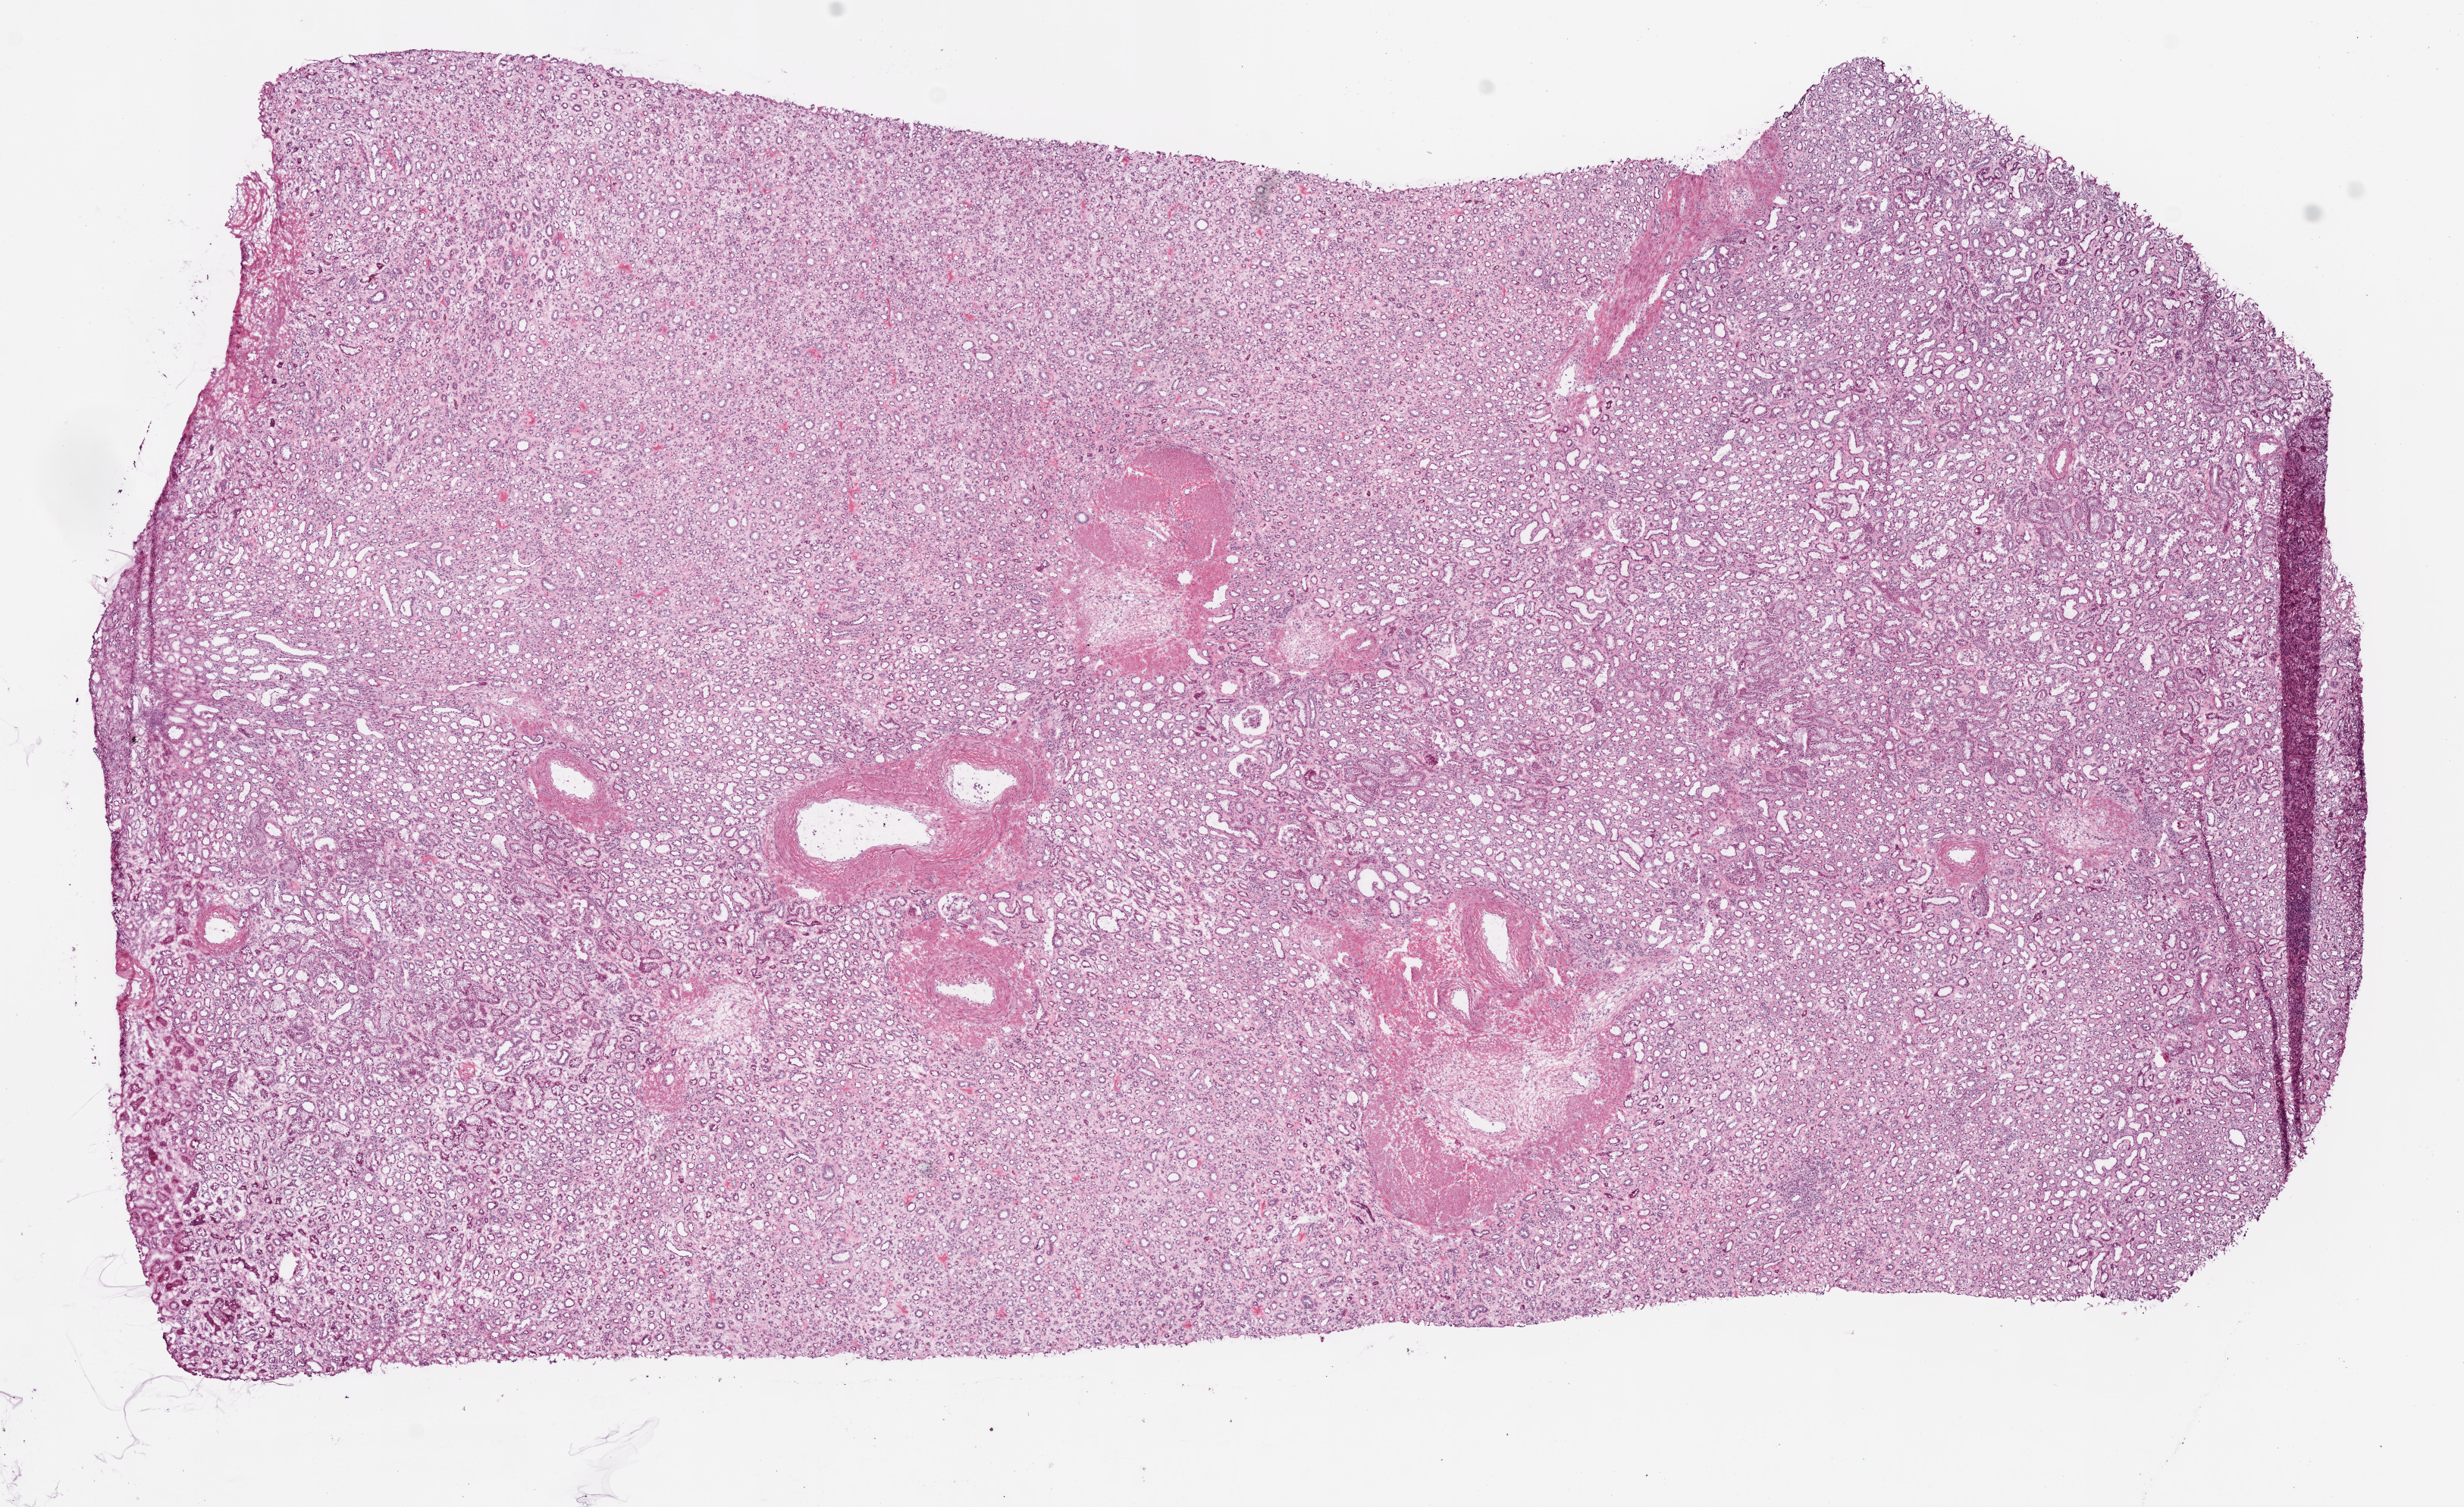
H&E-stained whole-slide image, a low-resolution overview of the entire scanned area, about 13.0 x 8.0 mm (acquisition: 20x scan); frozen section from the bottom of the tissue portion; solid tissue normal (non-tumour tissue) sample from the kidney. Patient: female, age at initial diagnosis 66 years.
* this section: solid tissue normal sample (biorepository sample class)
* patient diagnosis: Clear cell adenocarcinoma, NOS